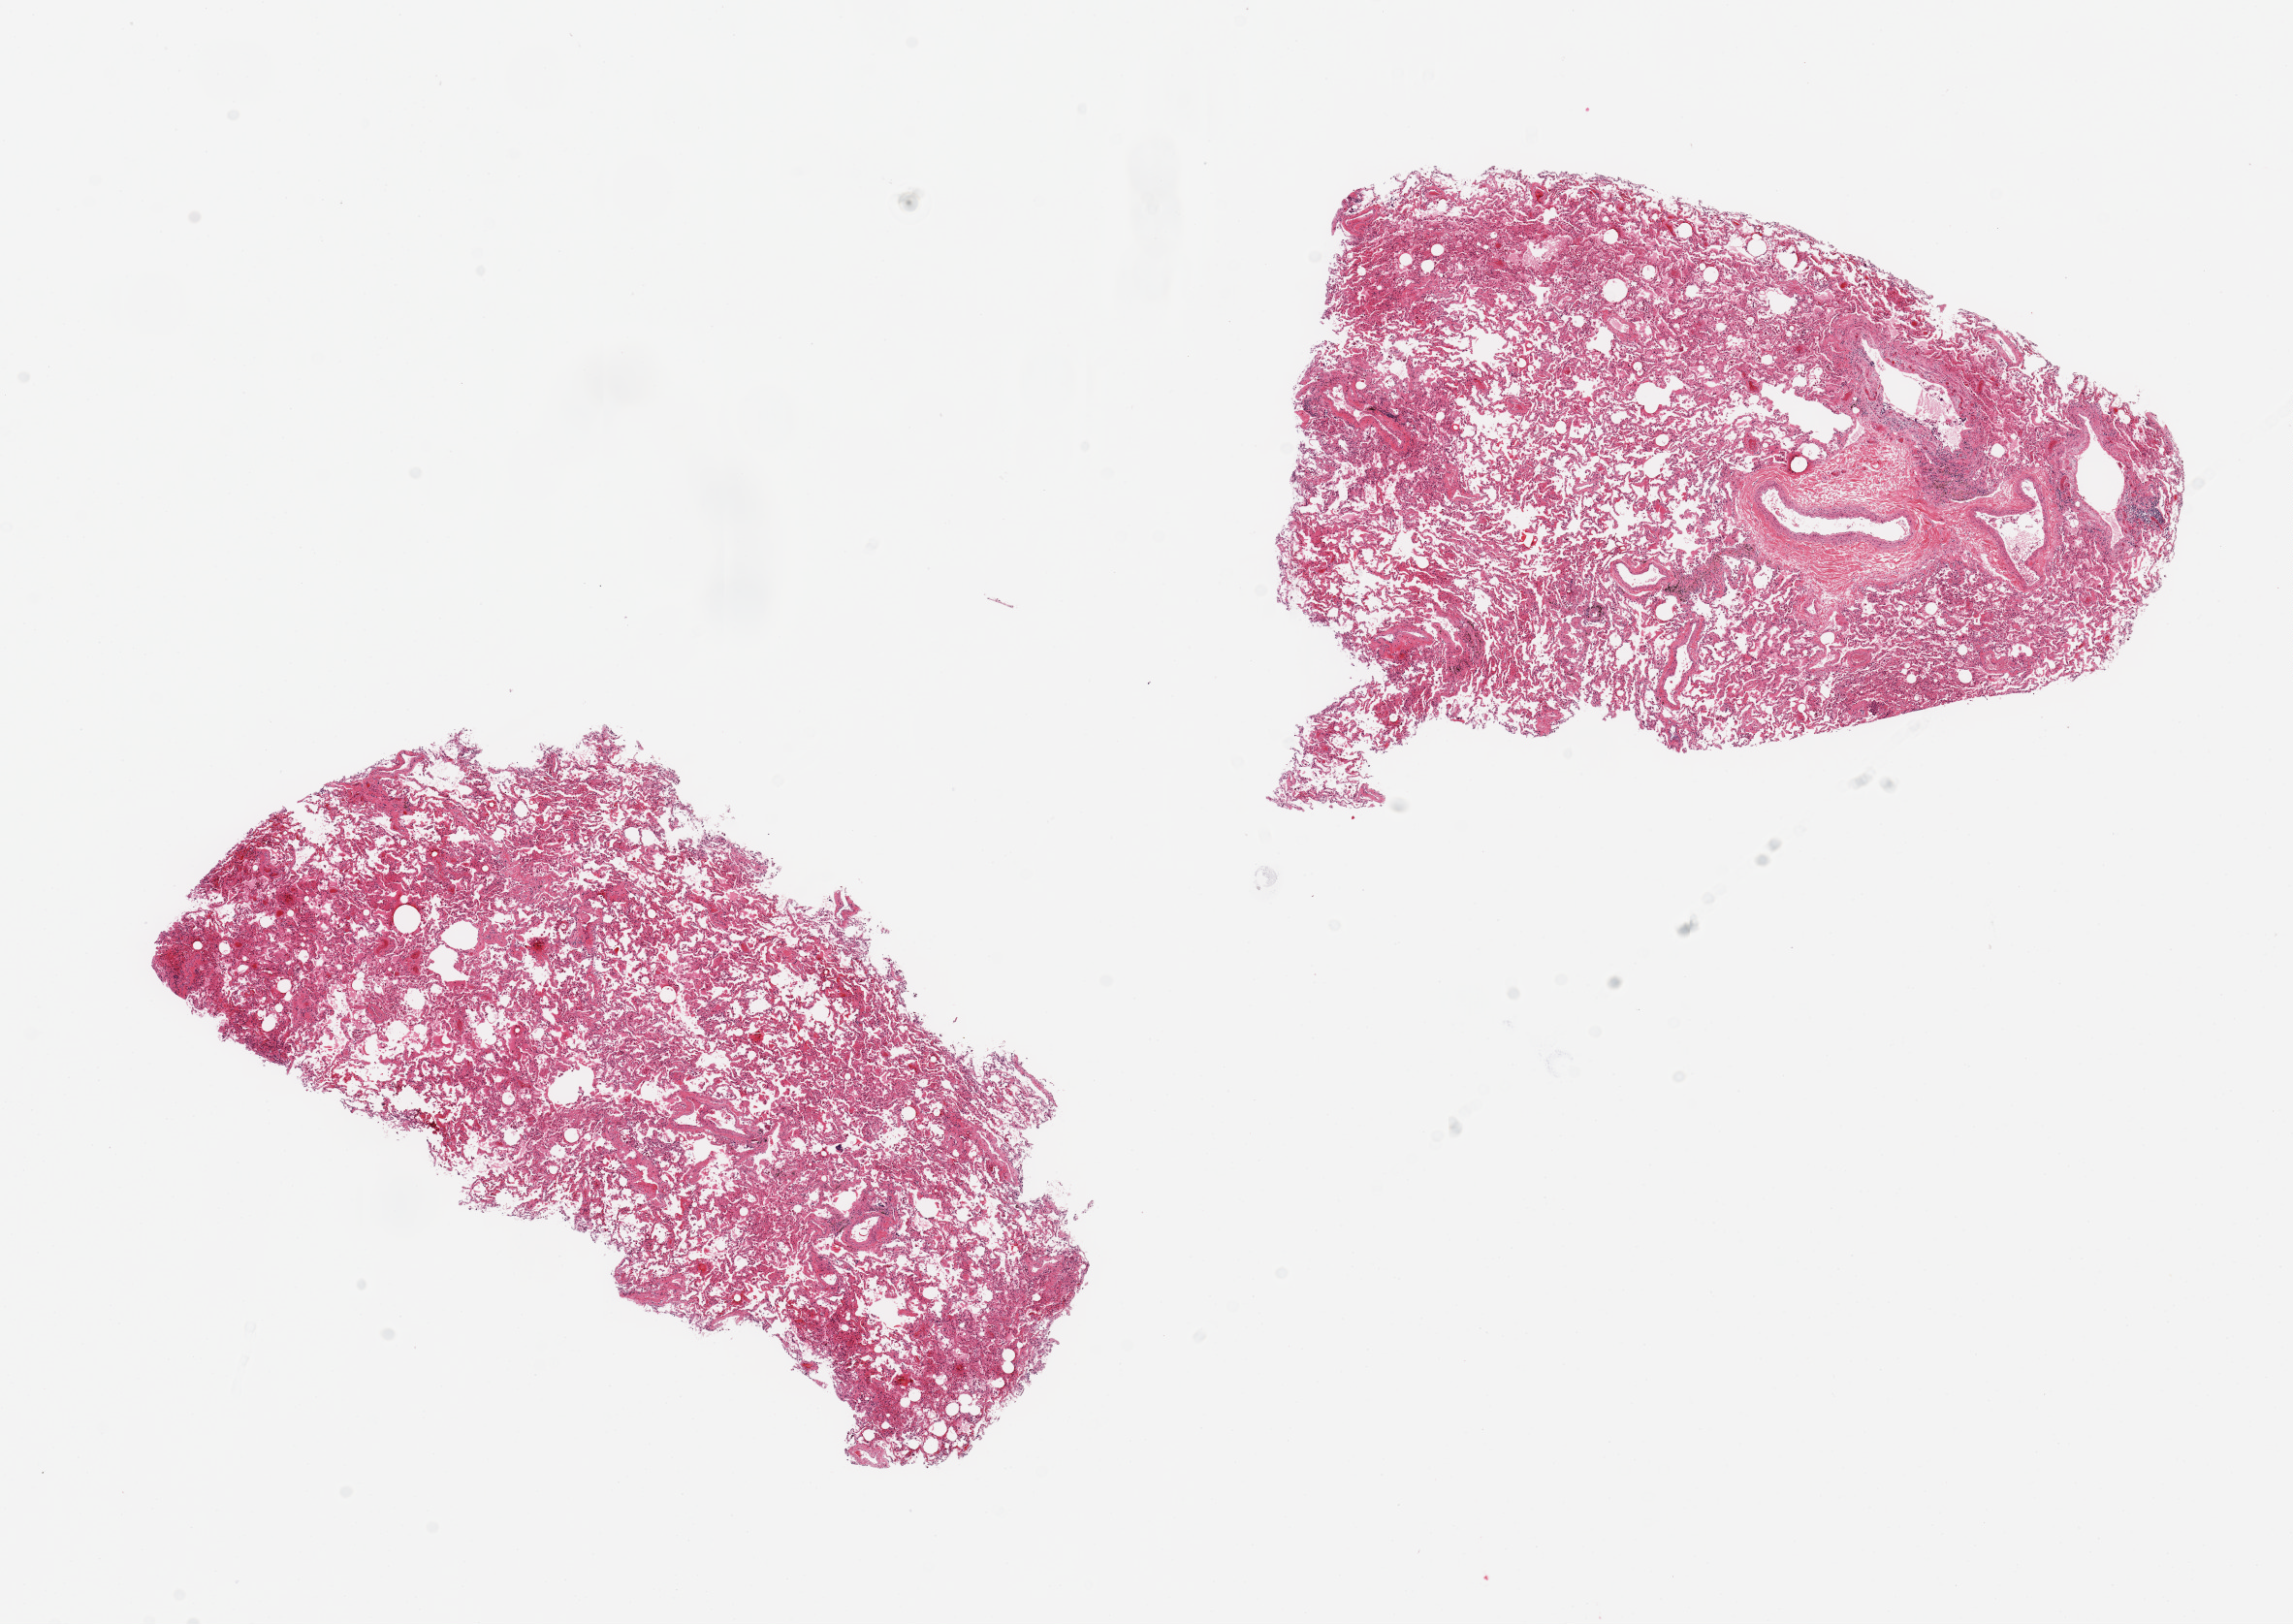
Whole-slide image, H&E stain — low-resolution overview of the scanned area, about 18.7 x 13.2 mm (slide scanned at 20x); PAXgene-fixed paraffin-embedded (PFPE) section; target tissue: lung; tissue donor sample.
* reviewer comment on this tissue sample: 2 pieces,~7x4mm; congested